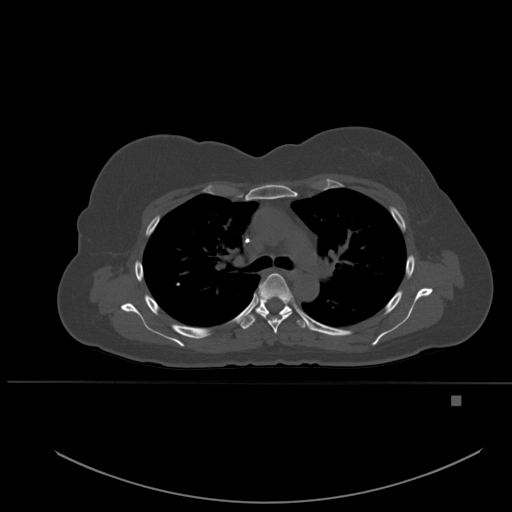
CT including the spine, one axial slice. Position 373 of 651 along the scan axis. Bone window (W 1800 / L 400 HU). 512 × 512 image matrix, field of view 443 × 443 mm. Patient: female, 49 years. Case-level facts recorded for this patient, not image findings: primary cancer: breast; vertebrae with lytic lesions (as recorded): L3, T12, L4.
Structures marked on this image (semi-automatically segmented with operator editing):
- T4 vertebra: bounding box [x1, y1, x2, y2] px = [258, 273, 293, 334]
- T5 vertebra: [240, 299, 305, 330]